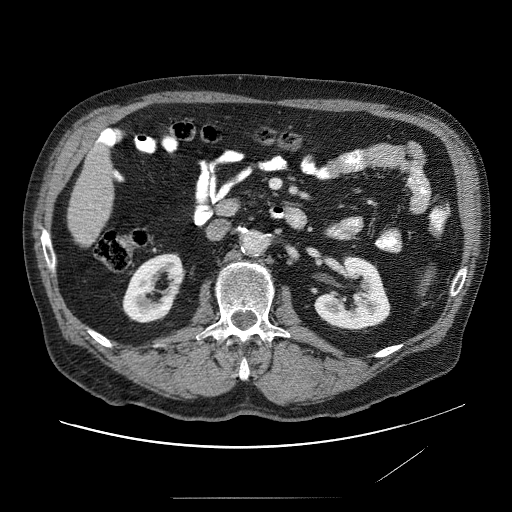
Contrast-enhanced abdominal CT (liver protocol), one axial slice. Reconstruction kernel STANDARD. 120 kVp. Soft-tissue window (W 400 / L 40 HU). 2.5 mm slice thickness. 512 × 512 image matrix, field of view 420 × 420 mm. Case-level facts recorded for this patient, not image findings: diagnosis: hepatocellular carcinoma (patient treated with transarterial chemoembolisation; whether this scan precedes or follows treatment is not stated here); TNM stage (as recorded): Stage-IVA; Child-Pugh class: A.
Annotated regions visible in this slice (semi-automatically segmented with operator editing):
- liver parenchyma outside the tumour (the mass and vessels are separate outlines, so this box may not span the whole liver): box from (x=66, y=126) to (x=120, y=248) px
- liver vessels: (x=84, y=127)–(x=114, y=221)